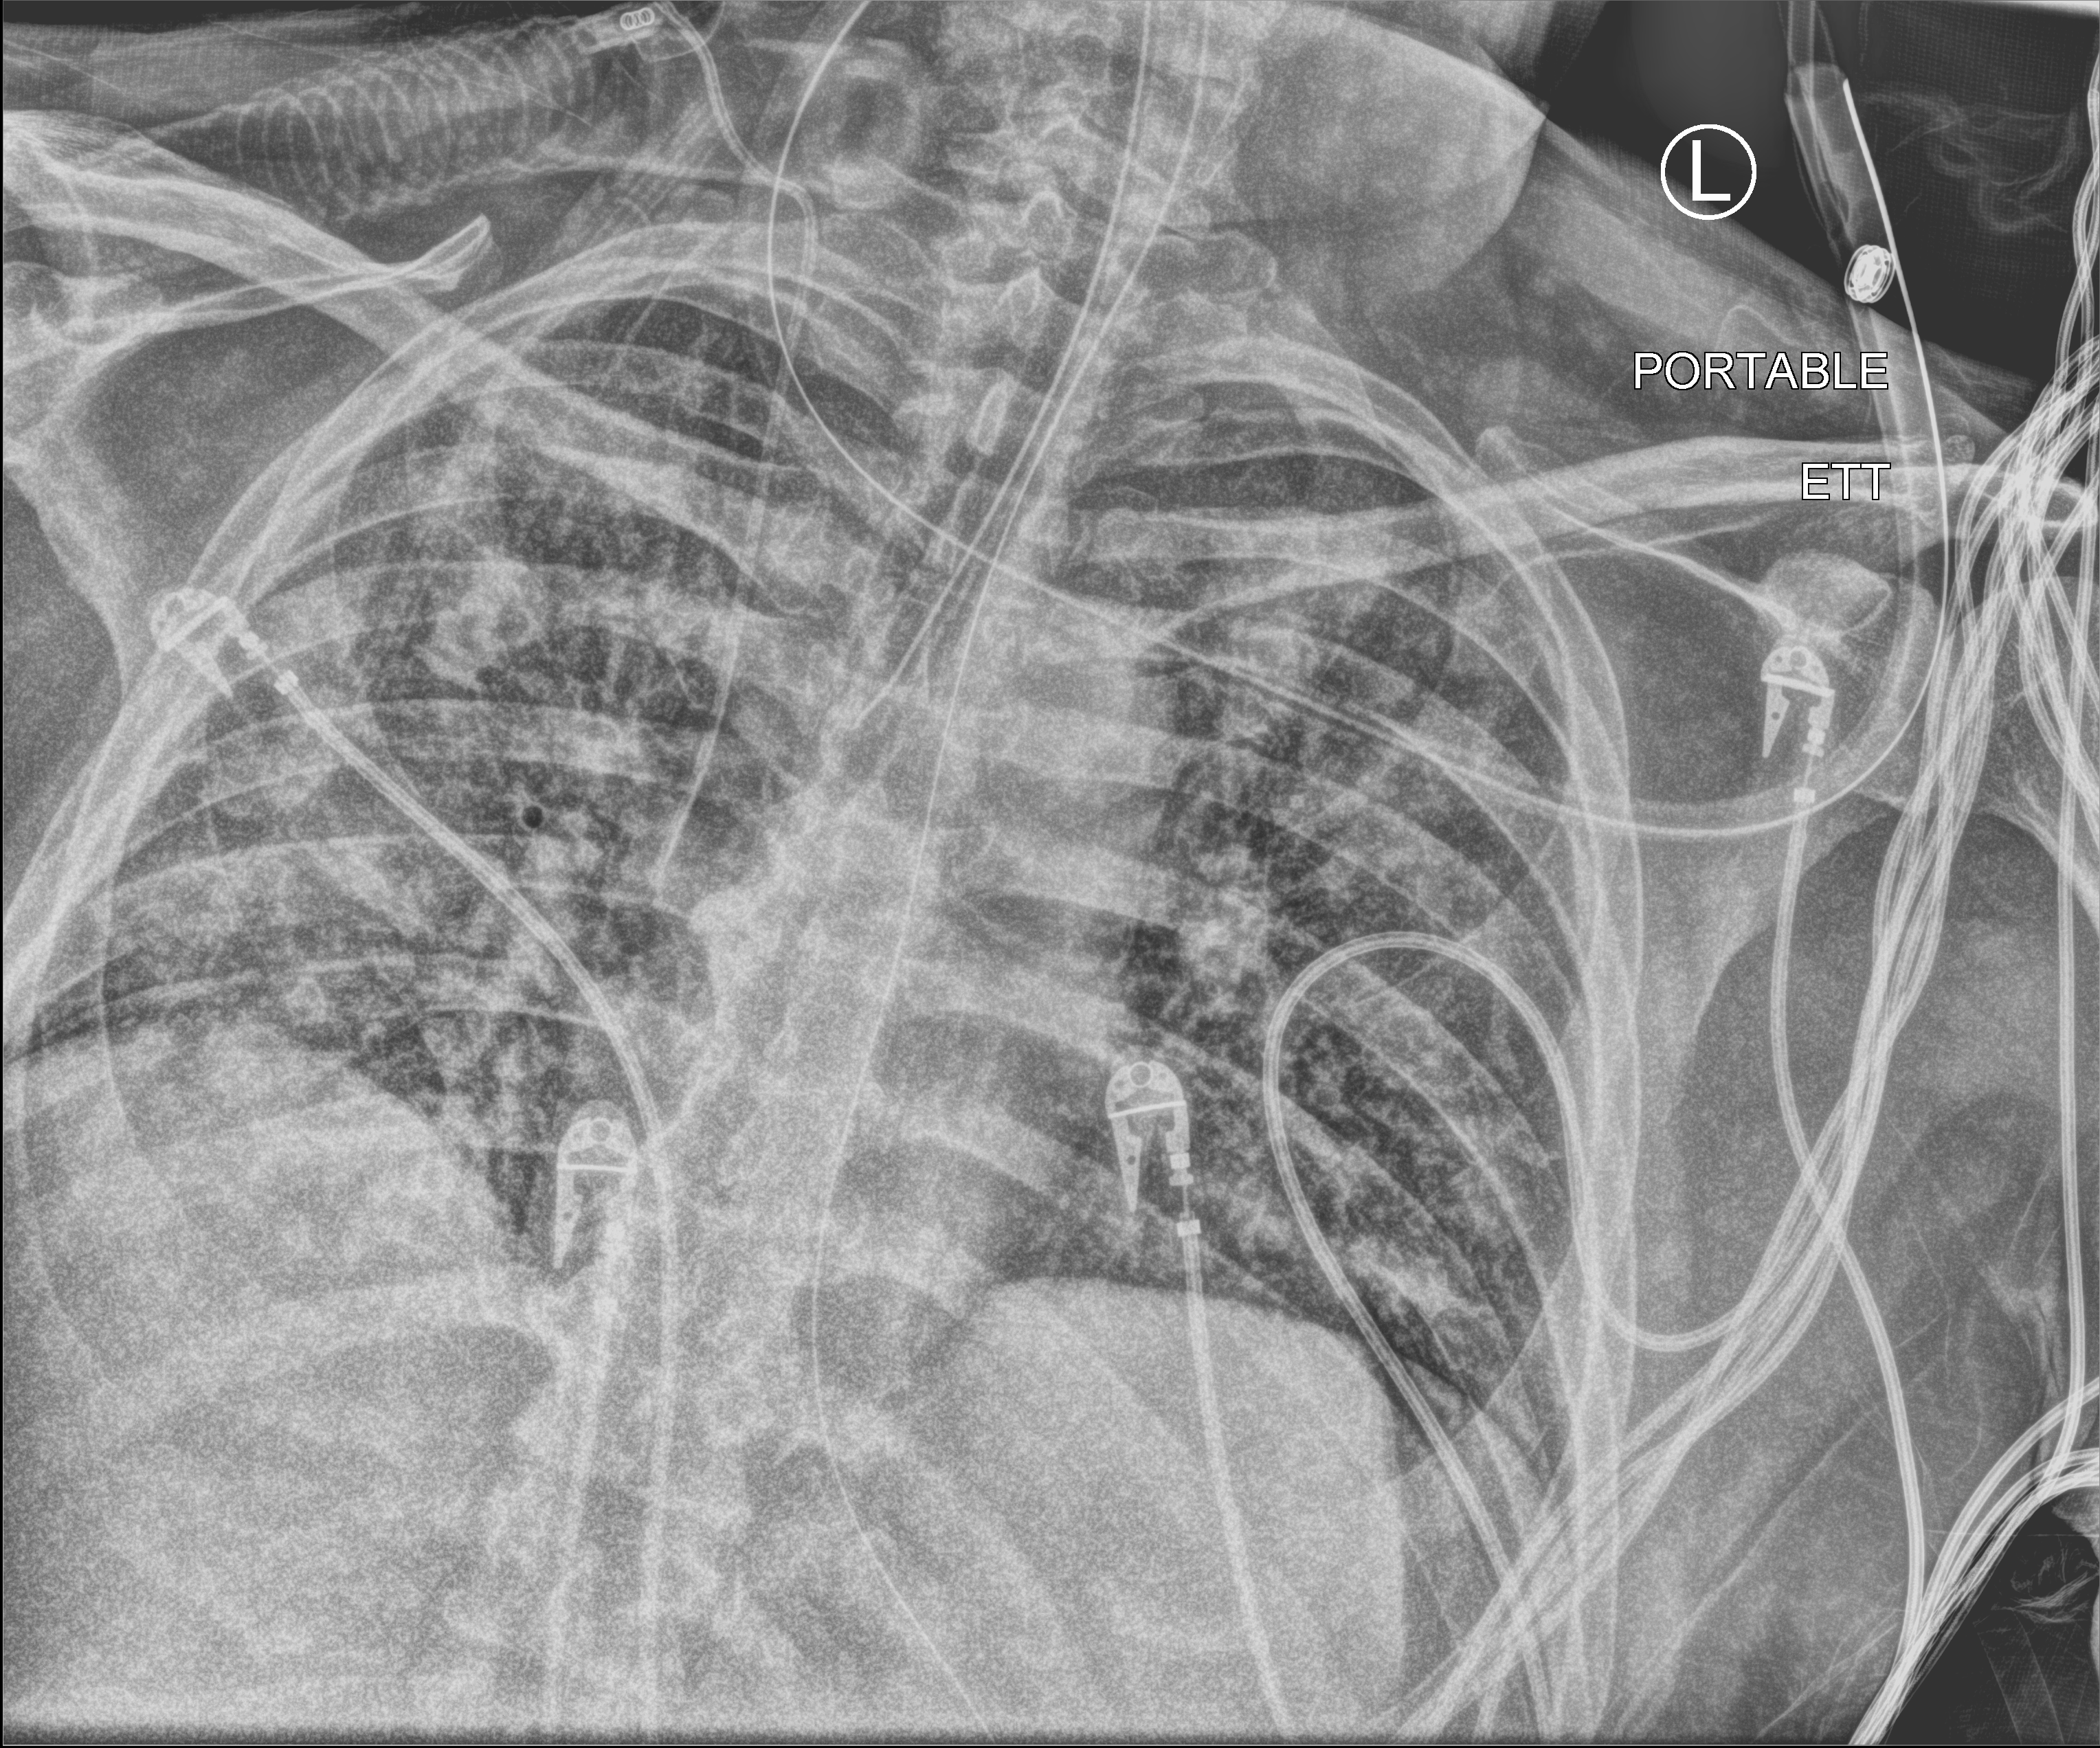
Bedside chest radiograph (computed radiography), anteroposterior (AP) projection. Patient hospitalised with COVID-19; male, aged 60–74 years.
From the hospital-stay record, not from the radiograph (when in the stay this image was taken is not recorded):
- mechanically ventilated during this hospital stay: yes